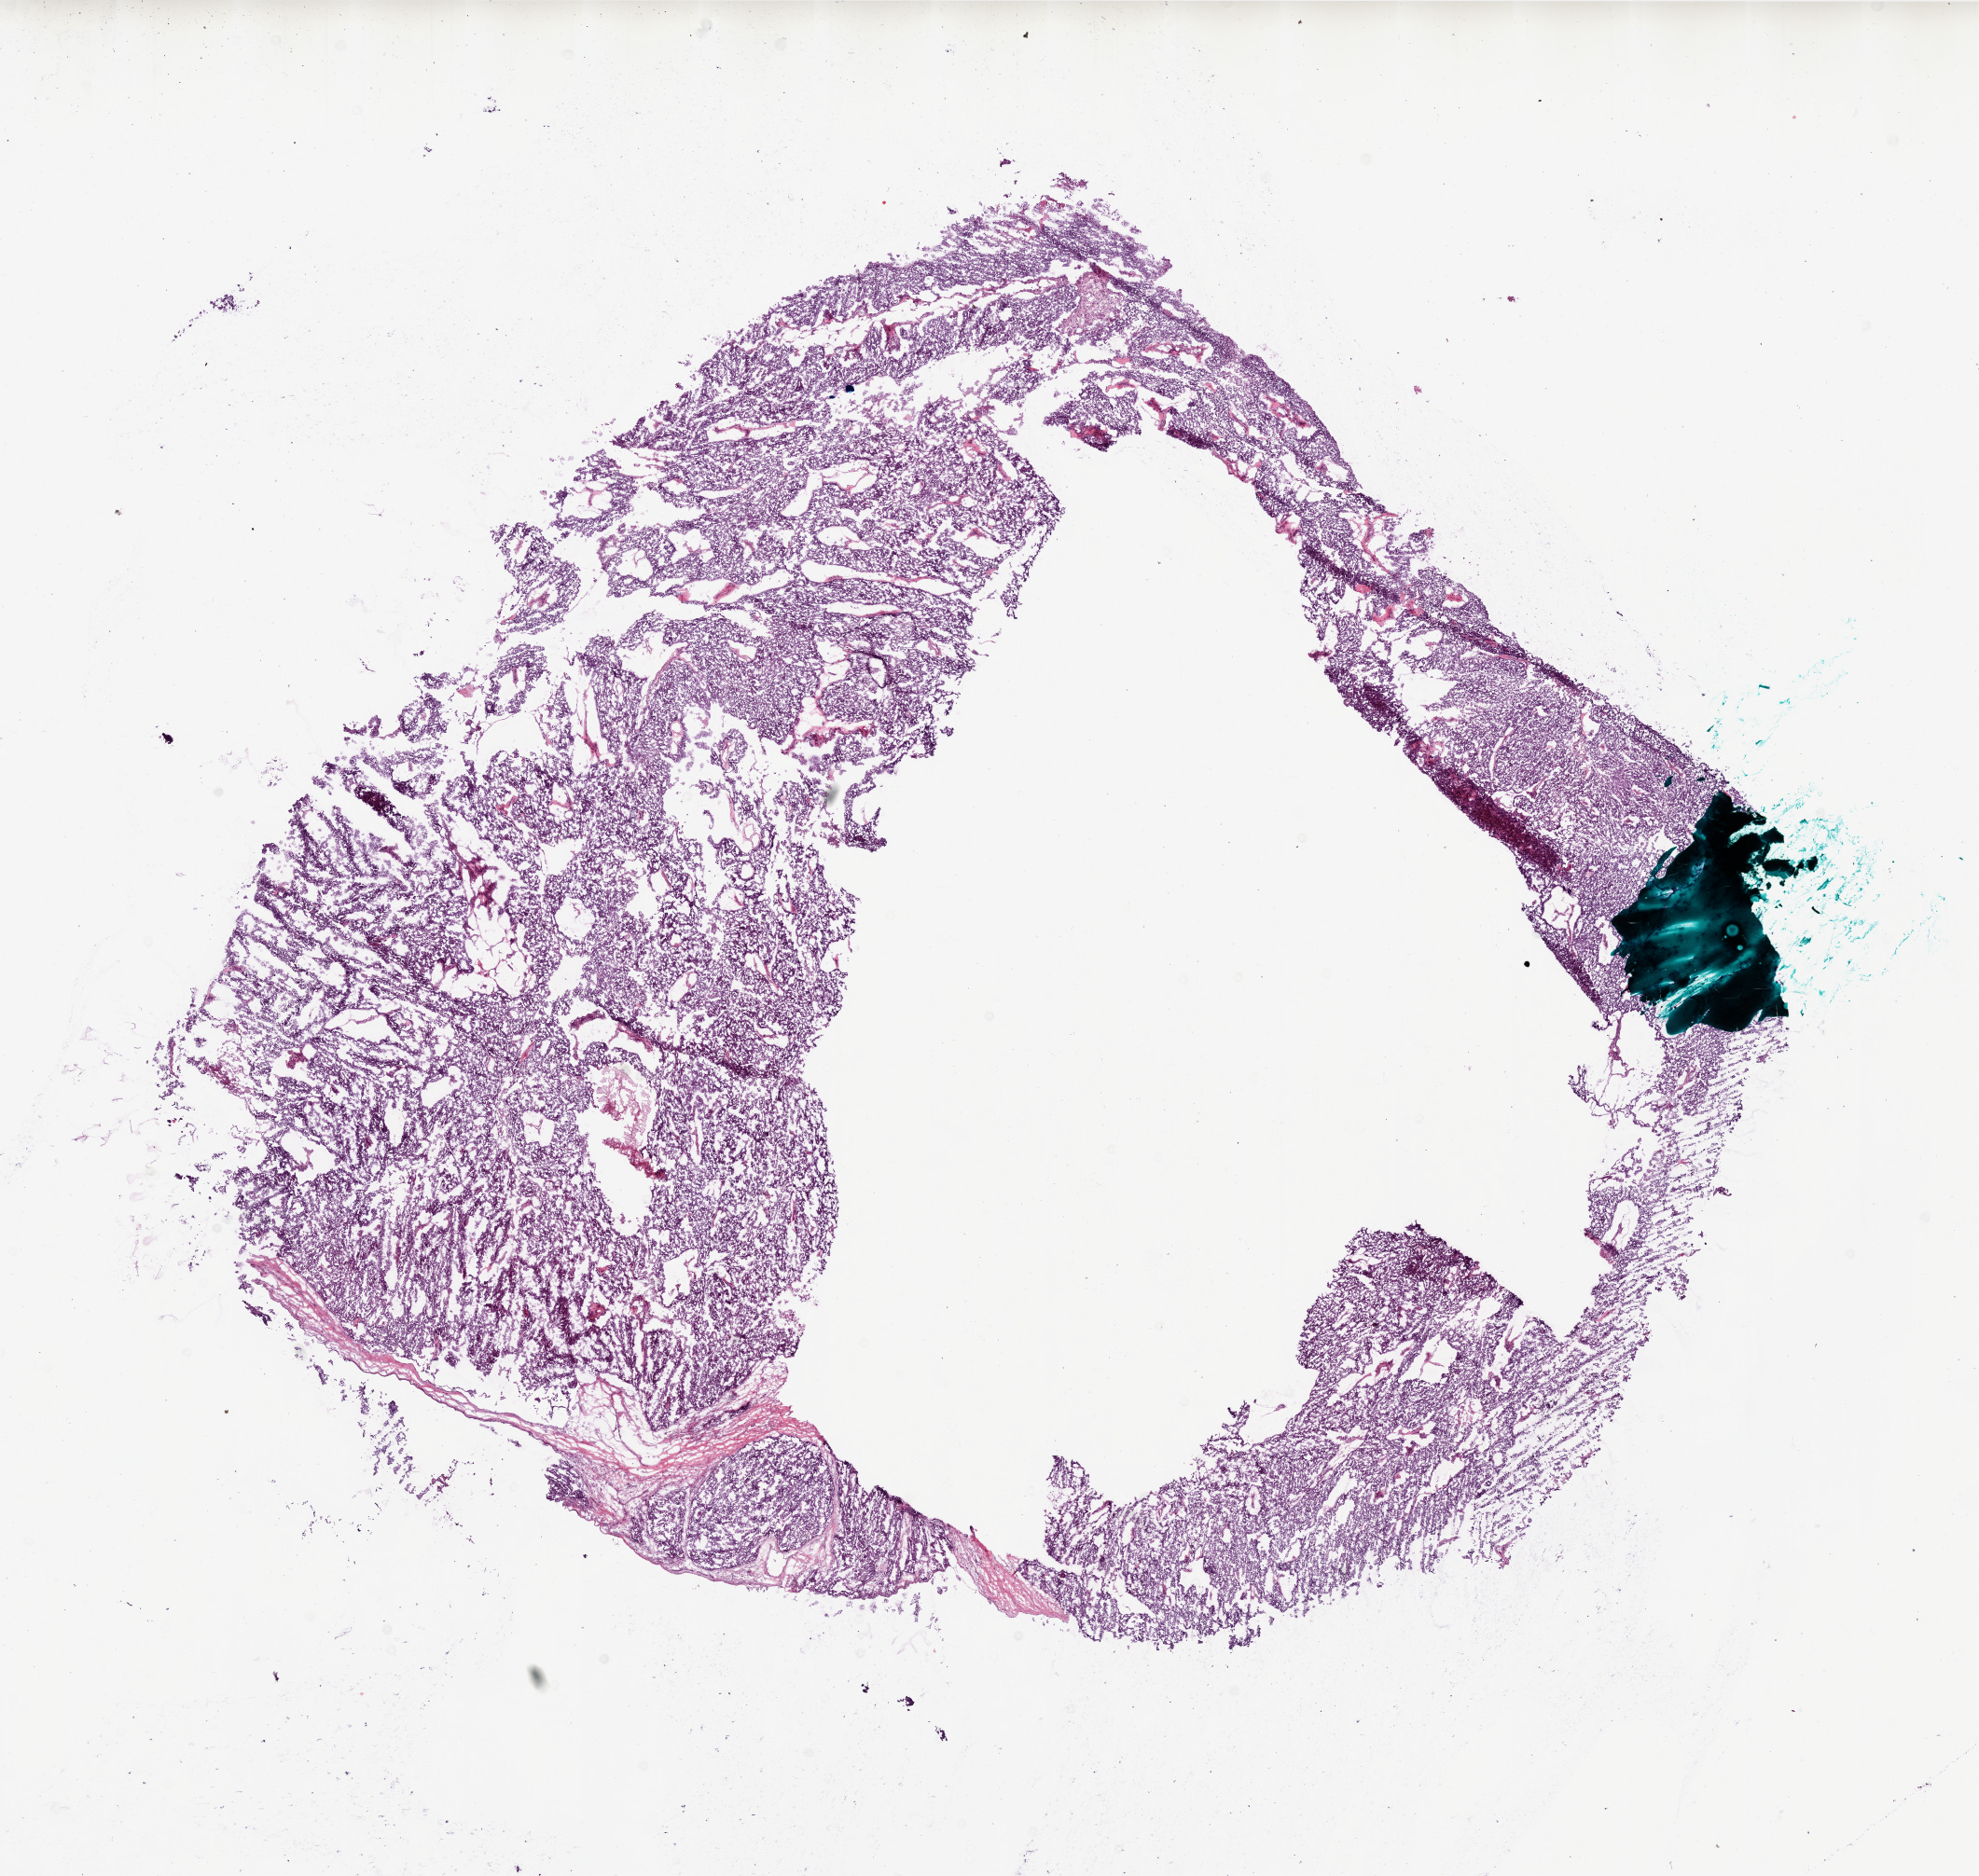
Whole-slide histology image, H&E, whole scanned area (about 17.0 x 16.1 mm, acquisition: 20x scan) shown as a low-resolution overview, frozen section, ovary, primary tumour sample. Female, age 73 years at initial diagnosis. Histologic grade: G3 (poorly differentiated). Composition of this section per pathologist review: tumour cells 94%, tumour nuclei 95%, normal cells 5%, stromal cells 0%, necrosis 1%.
- laterality: bilateral
- FIGO stage: IV
- histologic diagnosis: Serous cystadenocarcinoma, NOS